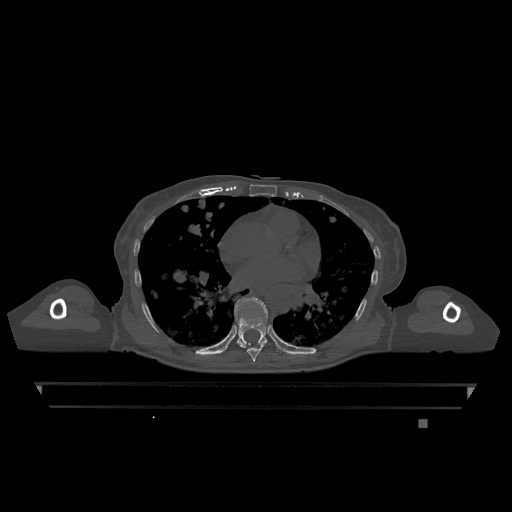
CT including the spine, one axial slice. Position 714 of 1317 along the scan axis. Bone window (W 1800 / L 400 HU). 0.5 mm slice thickness. 512 × 512 image matrix. Patient: female, 74 years. From the clinical record (not read from this slice): primary cancer: lung; vertebrae with lytic lesions (as recorded): T1, T4, T5, T6, L4, L5.
Annotated regions visible in this slice (semi-automatically segmented with operator editing):
- T7 vertebra: box from (x=239, y=344) to (x=264, y=362) px
- T9 vertebra: (x=234, y=298)–(x=268, y=346)